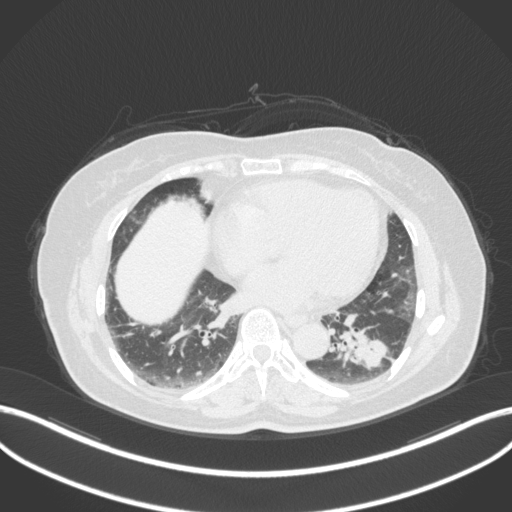
Chest CT, one axial slice. Slice 144 of 307 in the series (ordered by position). Reconstruction kernel B31f. Lung window (W 1500 / L -600 HU). 1 mm slice thickness. 512 × 512 image matrix. Female patient, age 59 years. Case-level facts recorded for this patient, not image findings: clinical TNM (as recorded): T2a N0 M0; histopathological grade: G2-3.
Annotated regions visible in this slice (rectangle marked by the reading radiologist):
- lung tumour (recorded histology: adenocarcinoma): box from (x=331, y=312) to (x=392, y=371) px